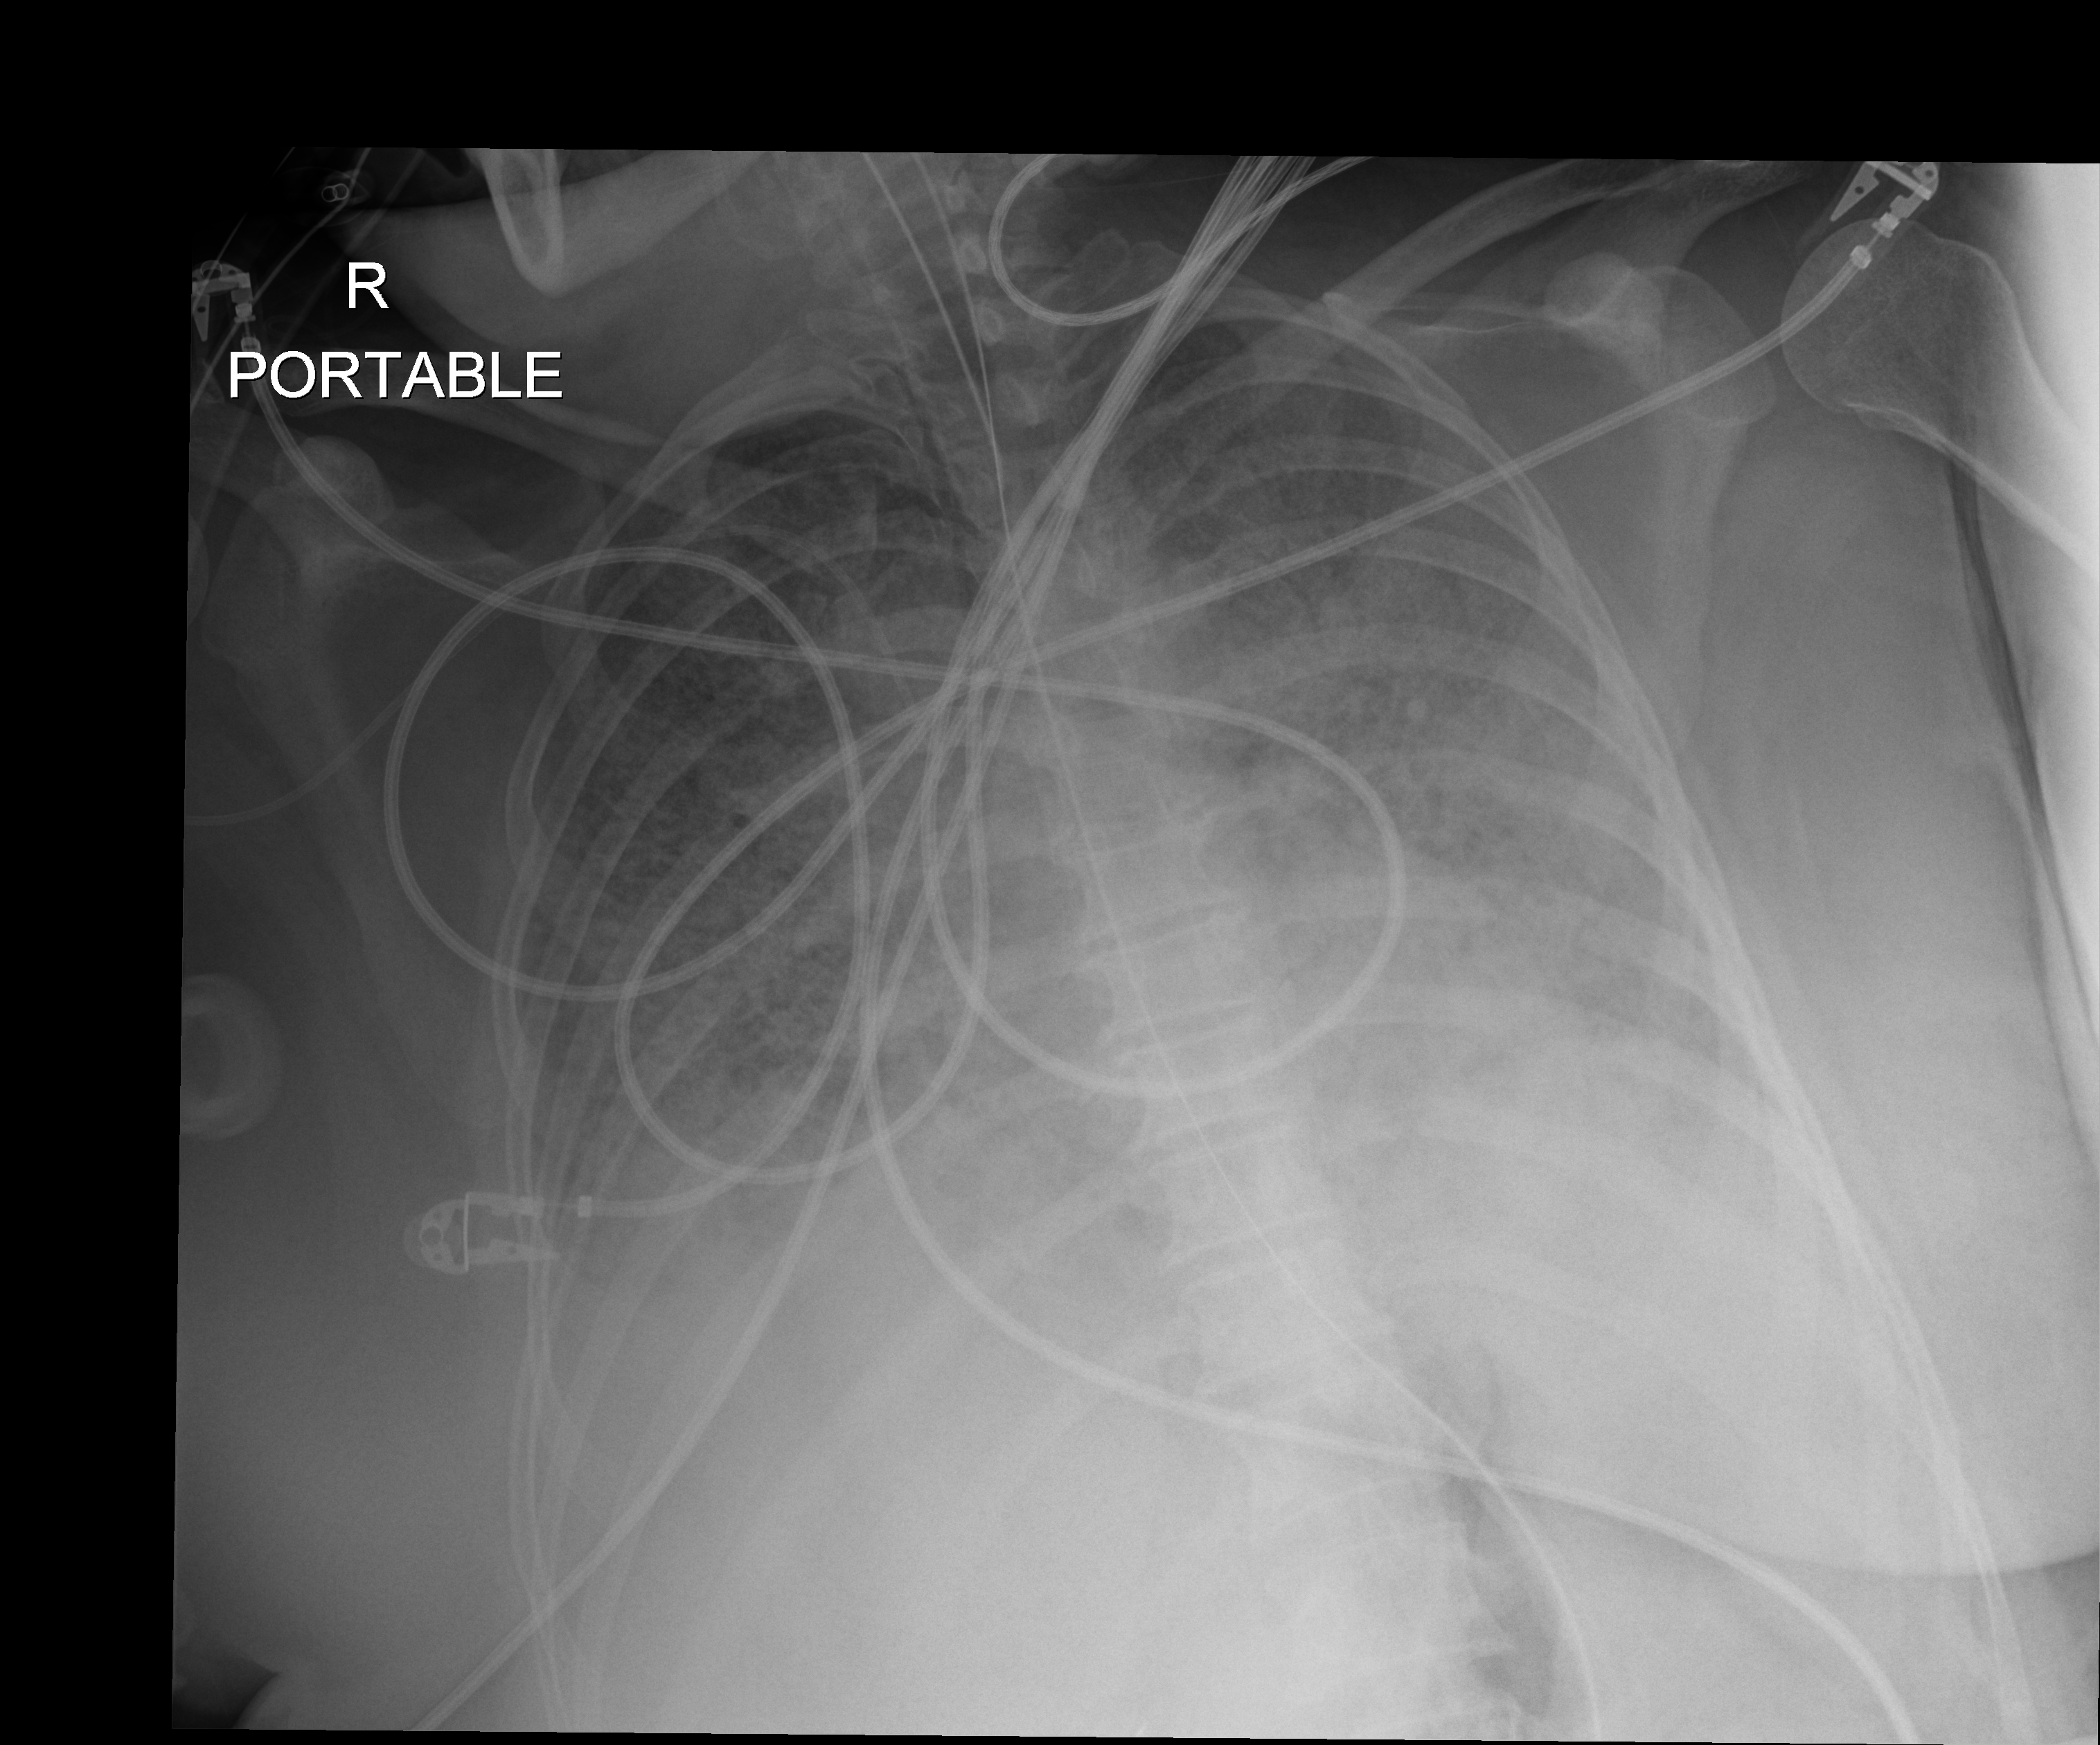
Portable chest radiograph; anteroposterior (AP) projection. Patient hospitalised with COVID-19; female, aged 18–59 years.
From the hospital-stay record, not from the radiograph (when in the stay this image was taken is not recorded): chronic kidney disease (admission record): no; admitted to intensive care during this hospital stay: yes; smoking status (admission record): never.